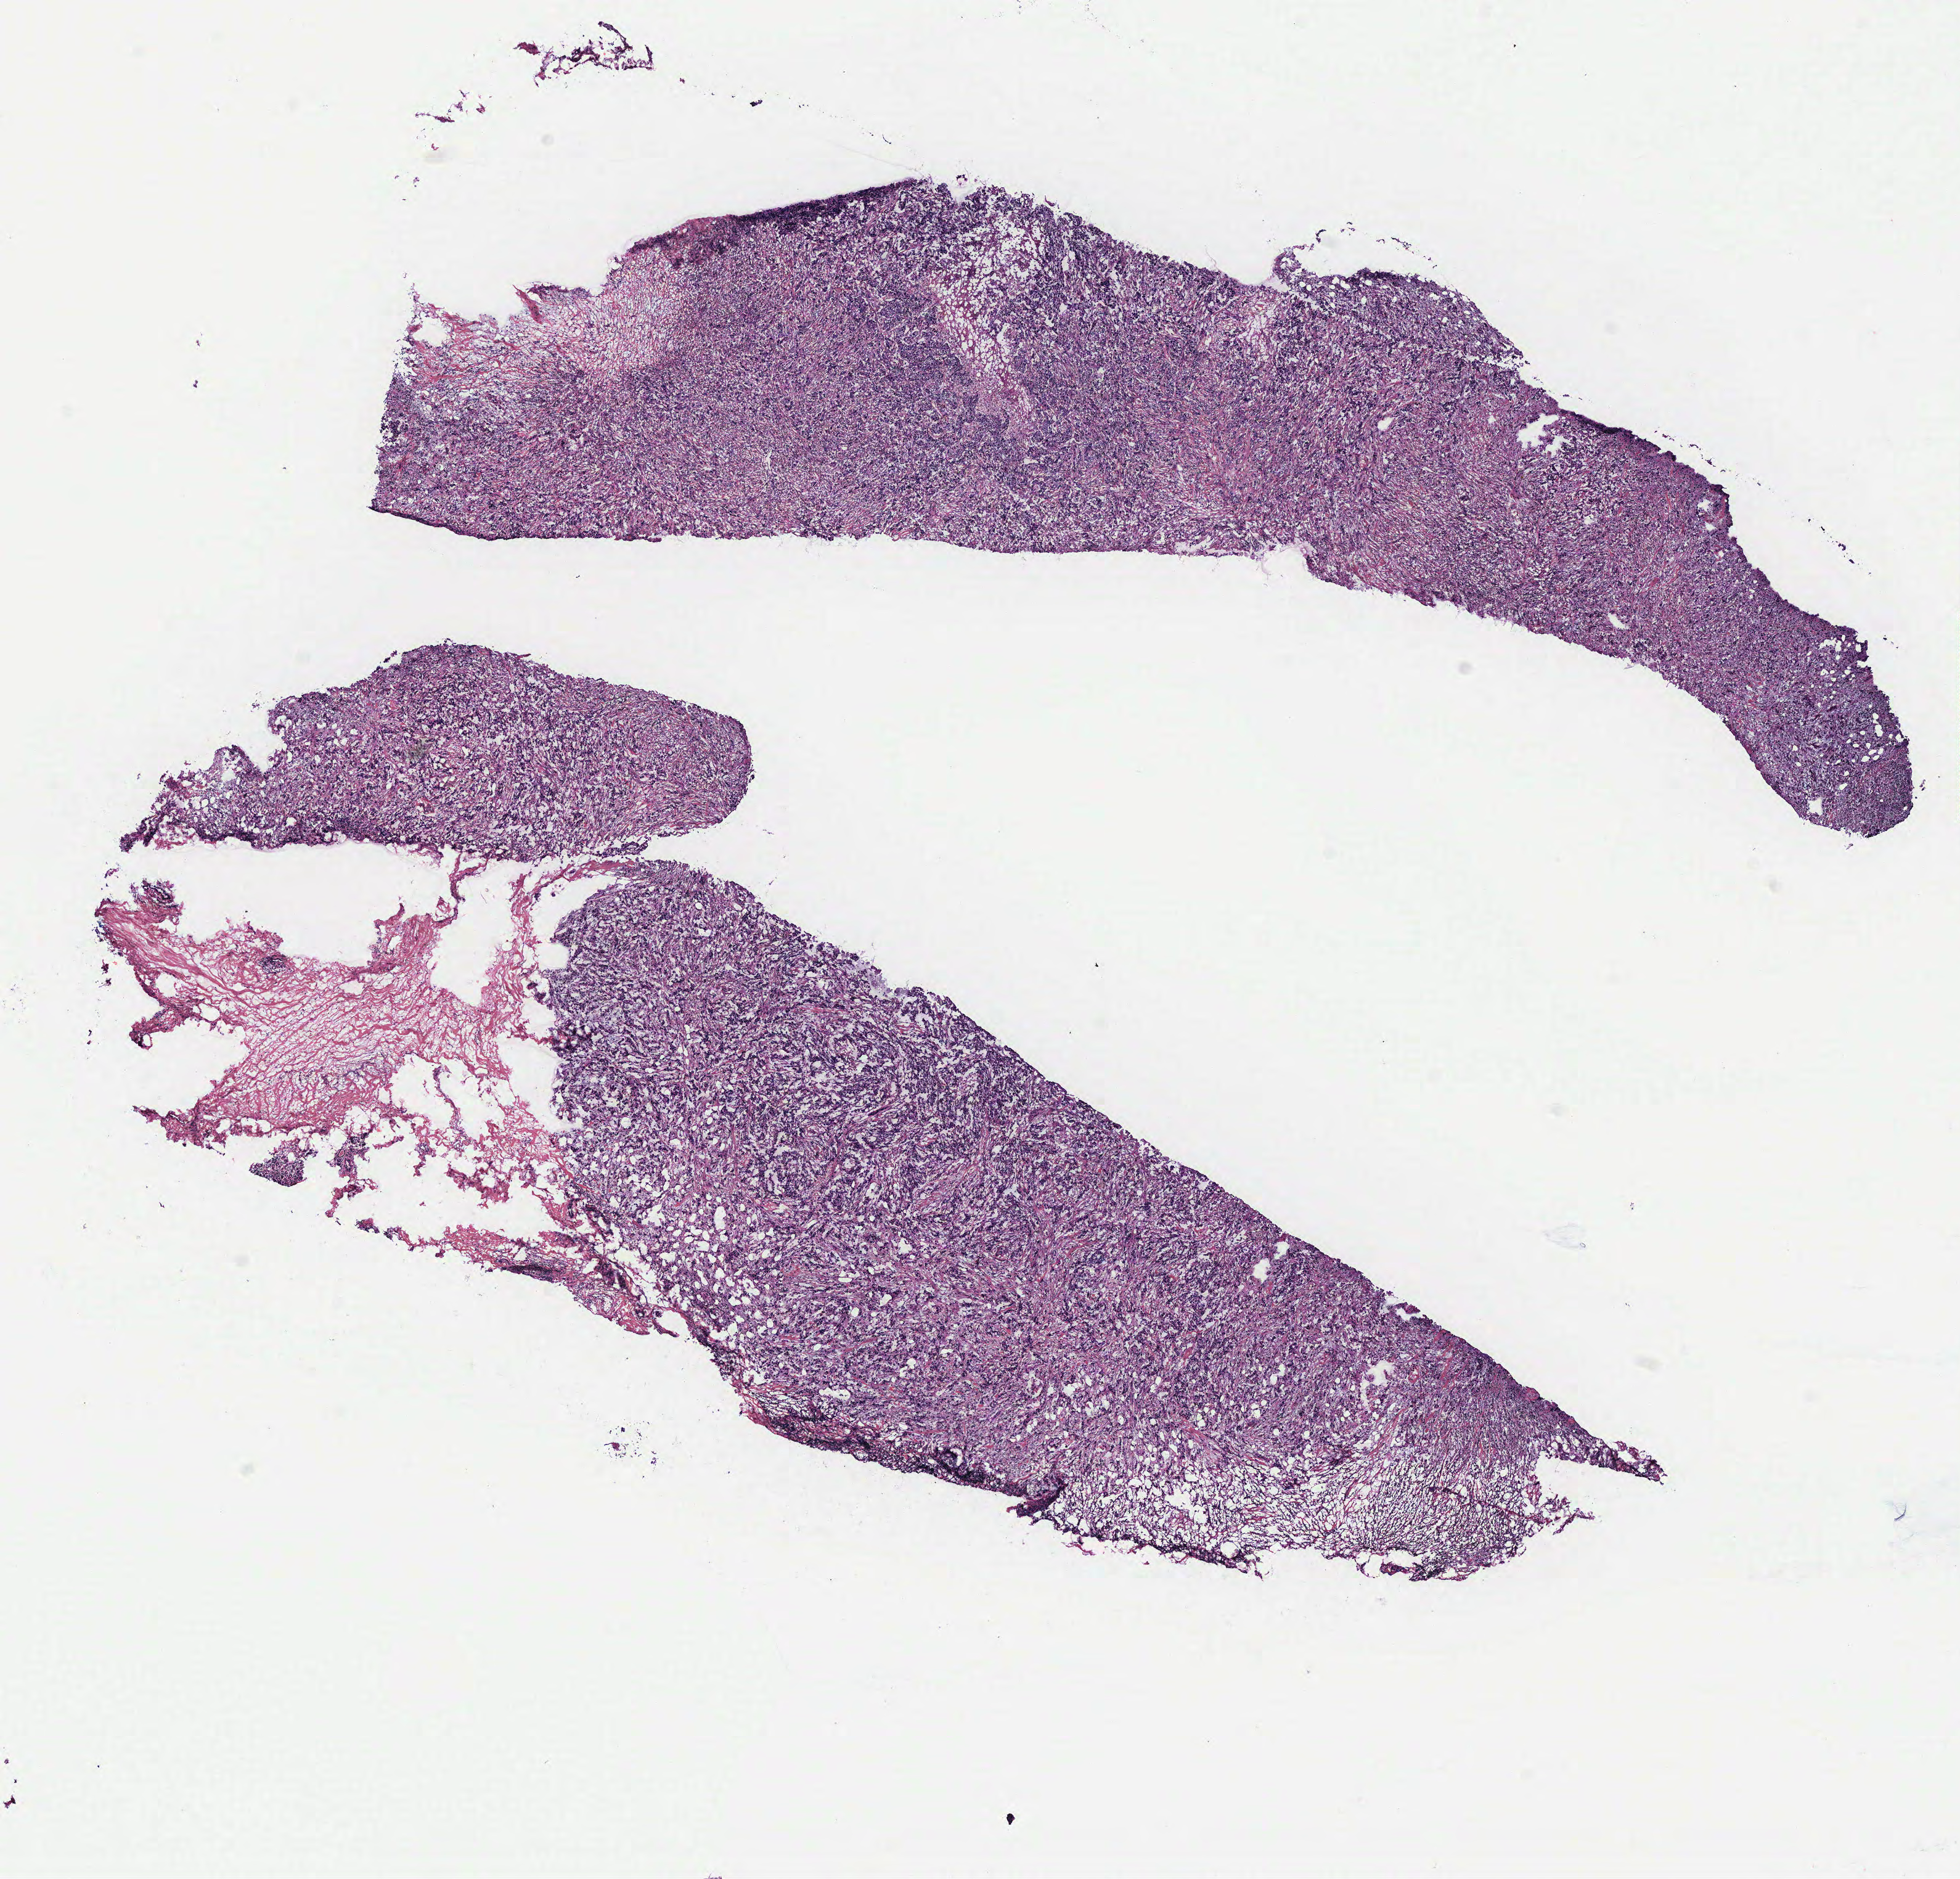
Hematoxylin and eosin (H&E) stained whole-slide image — low-resolution overview of the scanned area, about 12.7 x 12.2 mm (slide scanned at 40x), breast, tumour tissue. Patient: female, age 70 years.
- AJCC pathologic stage: IIB
- diagnosis: Infiltrating duct carcinoma, NOS